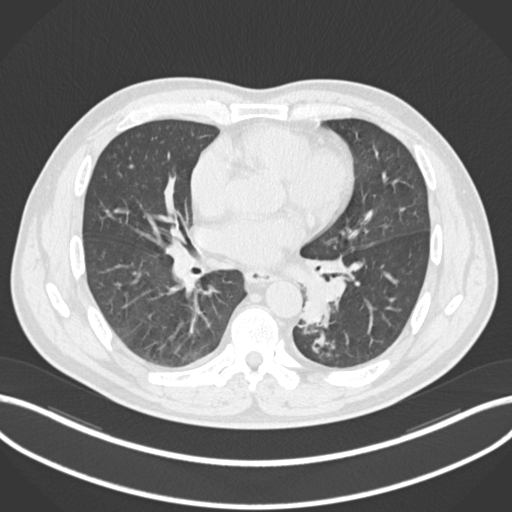
Chest CT, one axial slice; position 107 of 223 along the scan axis; reconstruction kernel B30f; 120 kVp; lung window (W 1500 / L -600 HU); 1 mm slice thickness; 512 × 512 image matrix, field of view 400 × 400 mm. Male patient, age 50 years. Case-level facts recorded for this patient, not image findings: clinical TNM (as recorded): T2a N3 M0.
Annotated regions visible in this slice (bounding box drawn by a radiologist):
- lung tumour (recorded histology: squamous cell carcinoma): bounding box (x1, y1, x2, y2) in pixels: (301, 269, 347, 328)